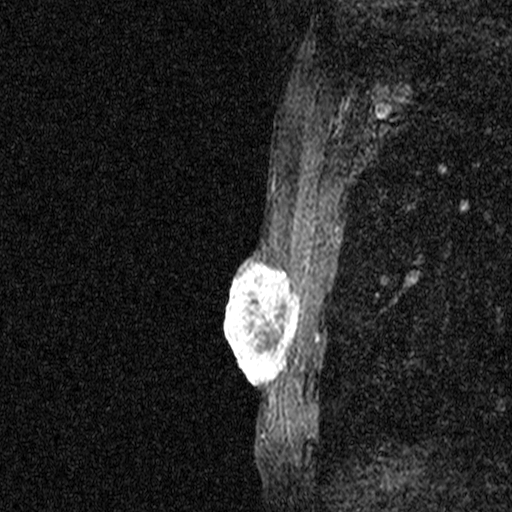
Breast MRI (dynamic contrast-enhanced), one sagittal slice. Slice 34 of 44 in the series (ordered by position). Dynamic contrast-enhanced study with each time point stored as its own series, time point 2 of 3 at this slice position (early post-contrast, ordered by acquisition time). 1.5 T. TE 4.5 ms, TR 11 ms. 2.05 mm slice thickness. 512 × 512 image matrix, field of view 200 × 200 mm. Female patient, age 44 years. From the clinical record (not read from this slice): setting: breast cancer imaged before/during neoadjuvant chemotherapy; receptor status: HR-positive, HER2-negative.
Outlined on this slice (semi-automatically segmented with operator editing):
- analysis volume of interest (the breast-tissue region the enhancement analysis was run in; not a lesion): box from (x=204, y=254) to (x=305, y=401) px
- tumour enhancement mask (voxels above the 90 % enhancement threshold inside the analysis volume of interest): (x=225, y=261)–(x=303, y=401)